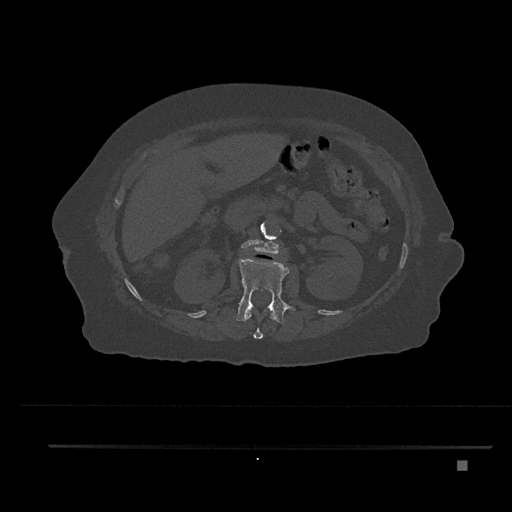
CT including the spine, one axial slice. 120 kVp. Bone window (W 1800 / L 400 HU). 0.5 mm slice thickness. 512 × 512 image matrix, field of view 437 × 437 mm. Female patient, age 76 years. Case-level facts recorded for this patient, not image findings: primary cancer: lung; vertebrae with lytic lesions (as recorded): T11, L3.
Outlined on this slice (semi-automatically segmented with operator editing):
- L1 vertebra: box from (x=236, y=257) to (x=295, y=325) px
- L2 vertebra: (x=241, y=239)–(x=280, y=255)
- T12 vertebra: (x=244, y=308)–(x=277, y=339)